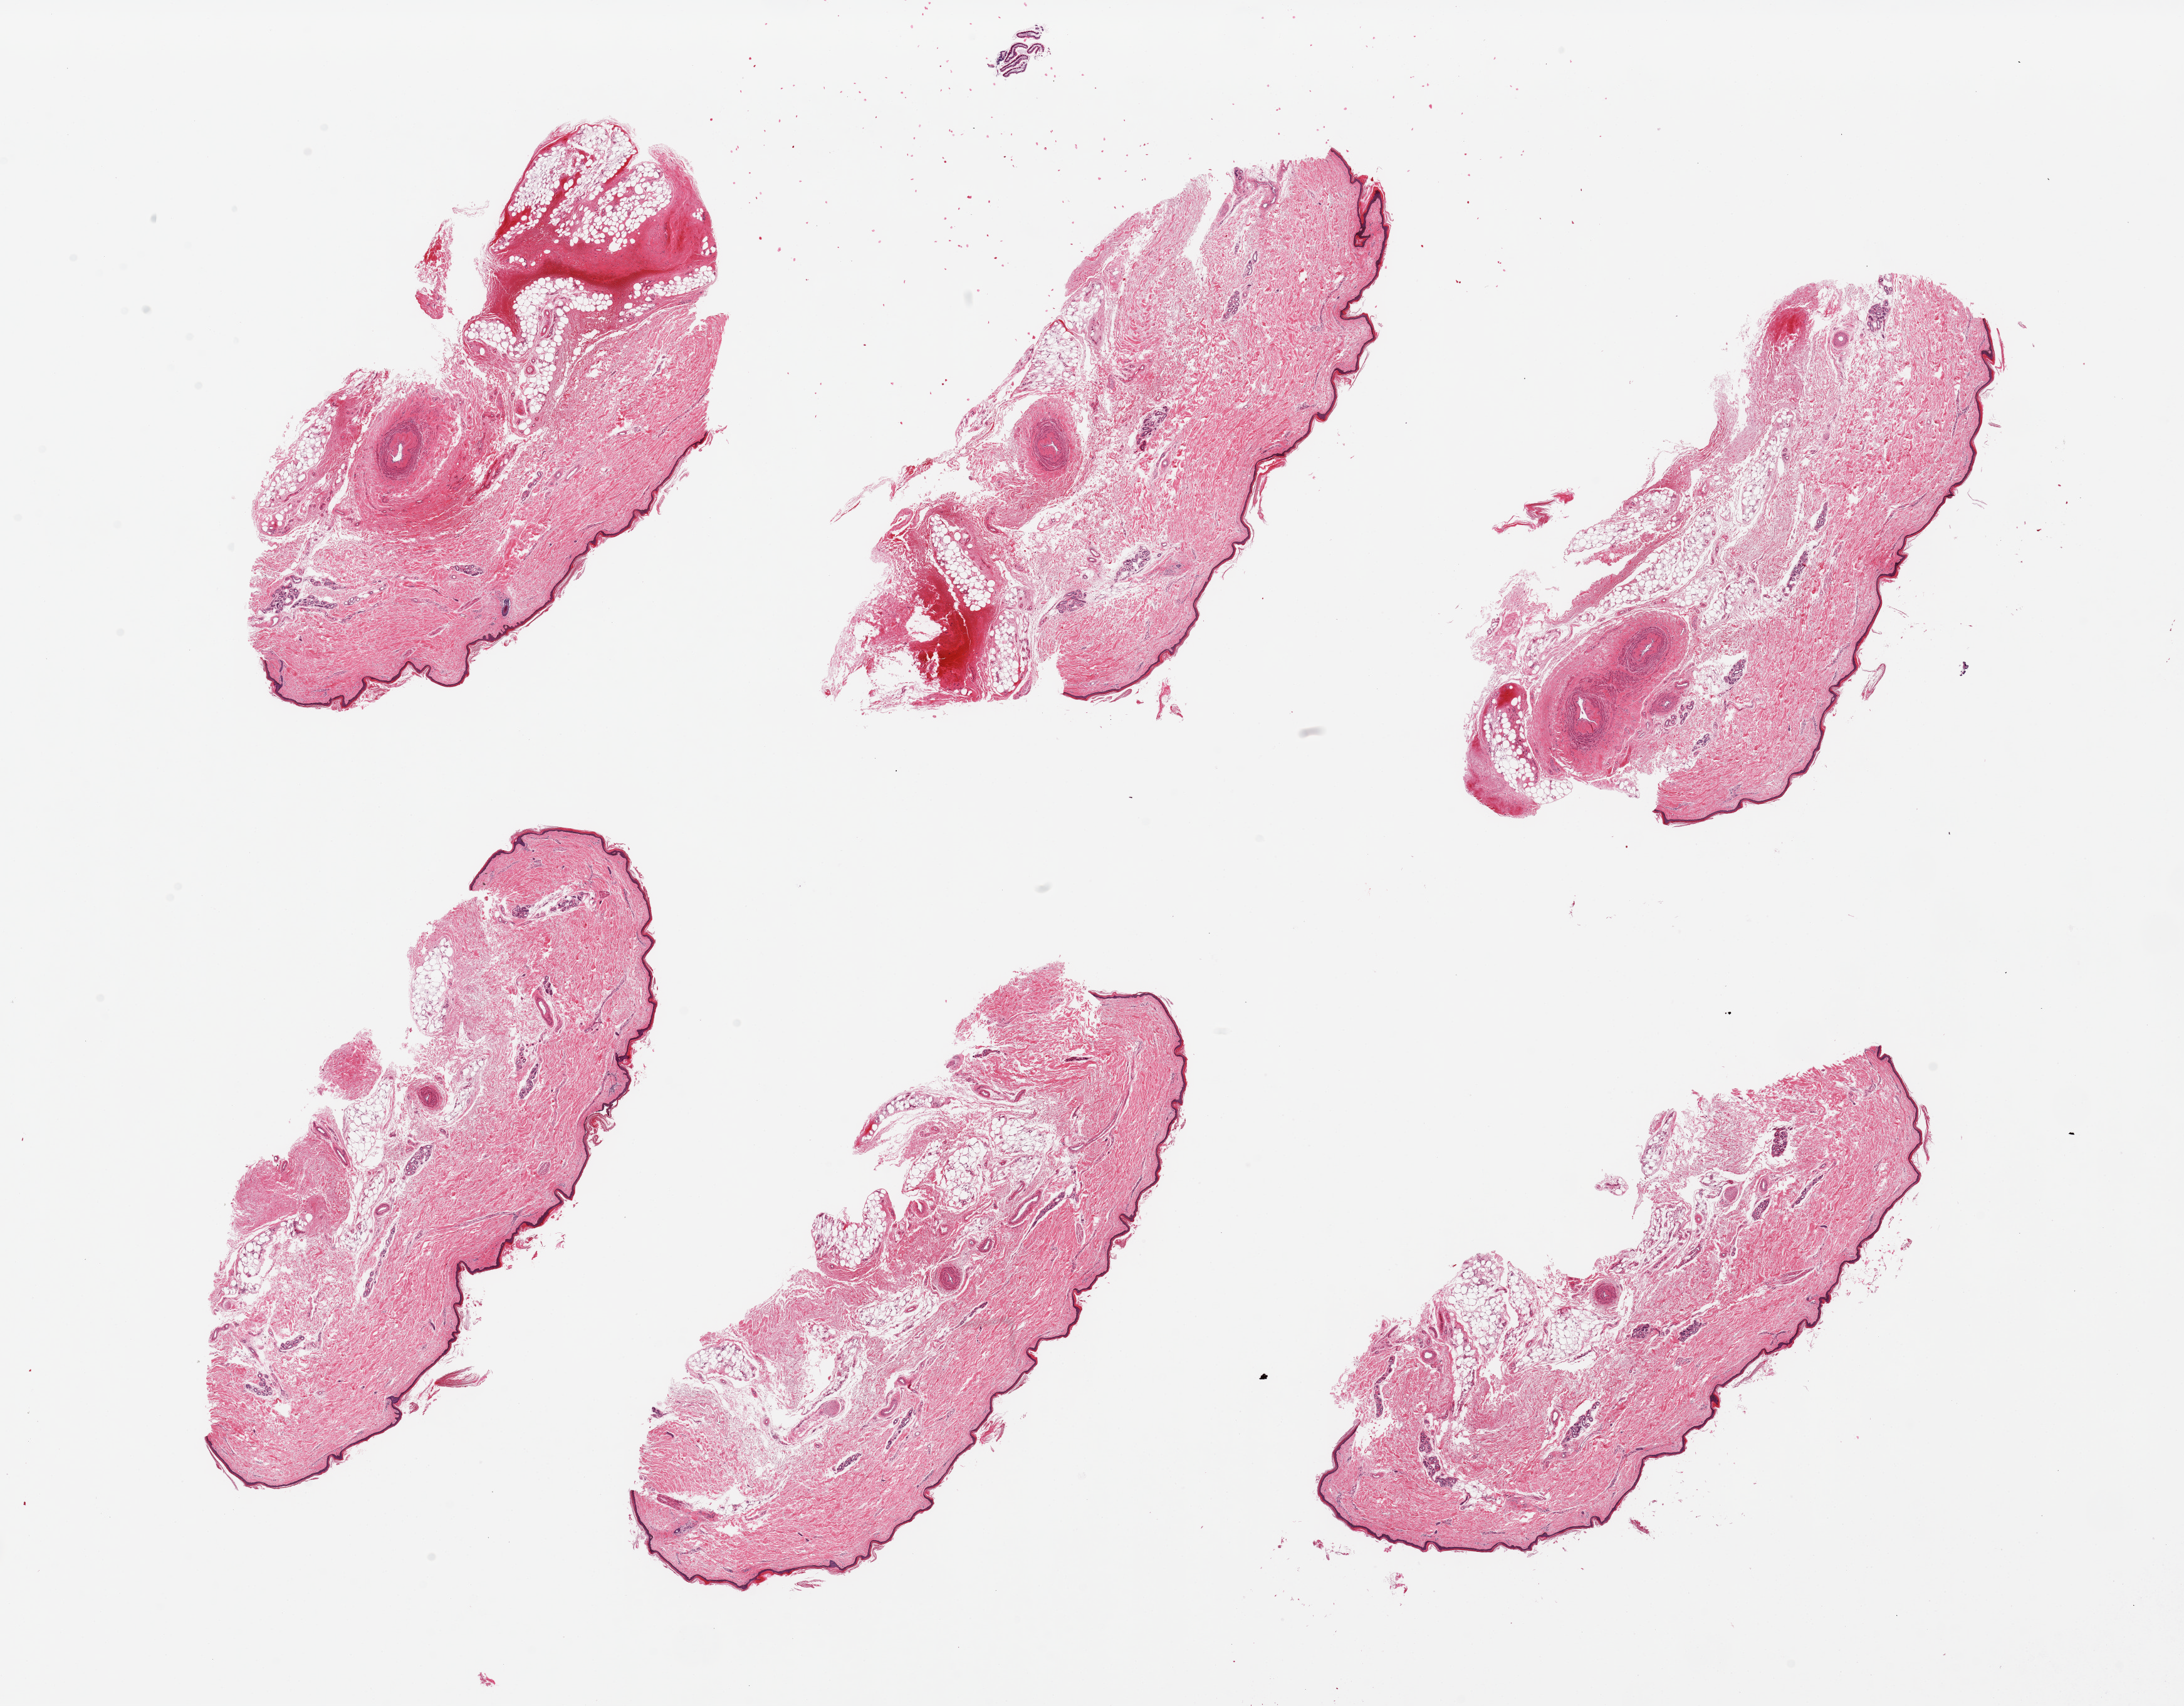
Digitized haematoxylin and eosin-stained section, brightfield — whole scanned area (about 27.6 x 21.5 mm, from a 20x scan) shown as a low-resolution overview; PAXgene-fixed, paraffin-embedded tissue; section of skin of lower leg (target tissue); tissue donor sample. Female donor.
- pathologist's review note for this sample: 6 pieces, up to 9x5mm; up to 2mm of subcutaneous adipose with several large vessels